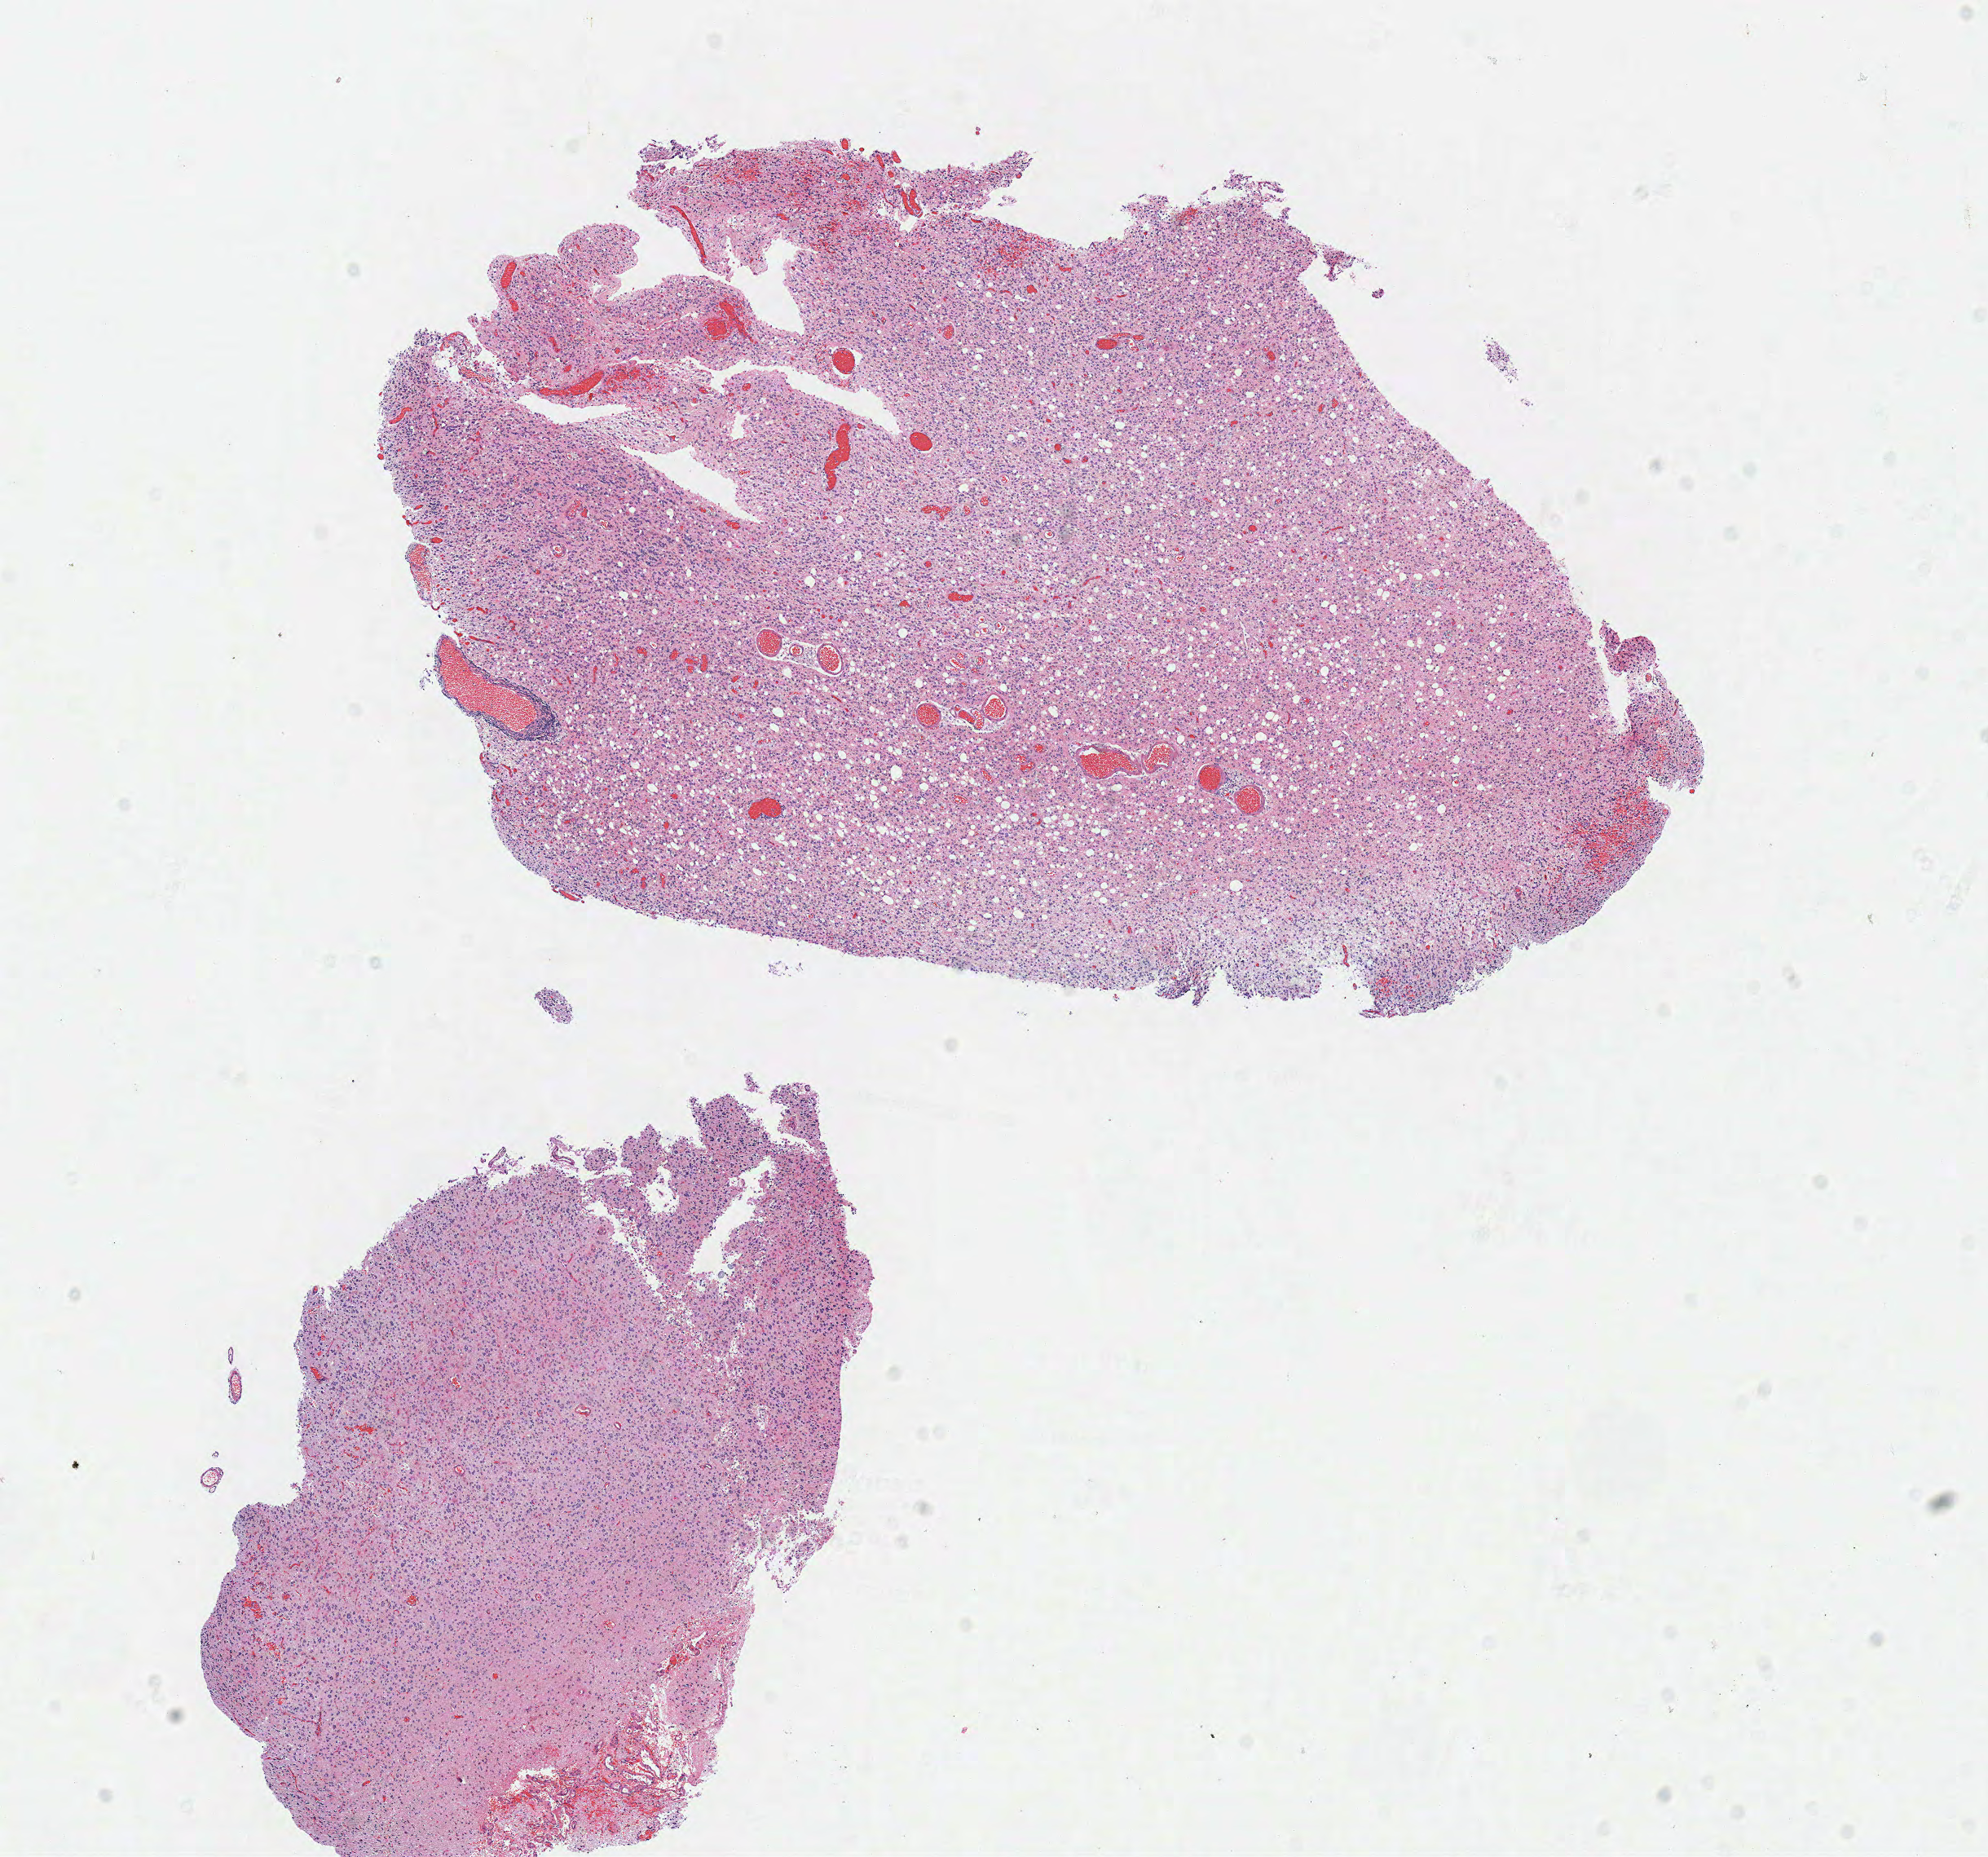
H&E-stained whole-slide image, low-resolution overview of the scanned area, about 9.6 x 9.0 mm. Frozen section from the top of the tissue portion. Sample: primary tumour, brain. Male, age 48 years at initial diagnosis. Histologic grade: G2 (moderately differentiated). Slide review estimates, as recorded: tumour cells 100%, tumour nuclei 80%, normal cells 0%, stromal cells 0%, necrosis 0%.
Laterality: left. Histologic diagnosis: Oligodendroglioma, NOS.